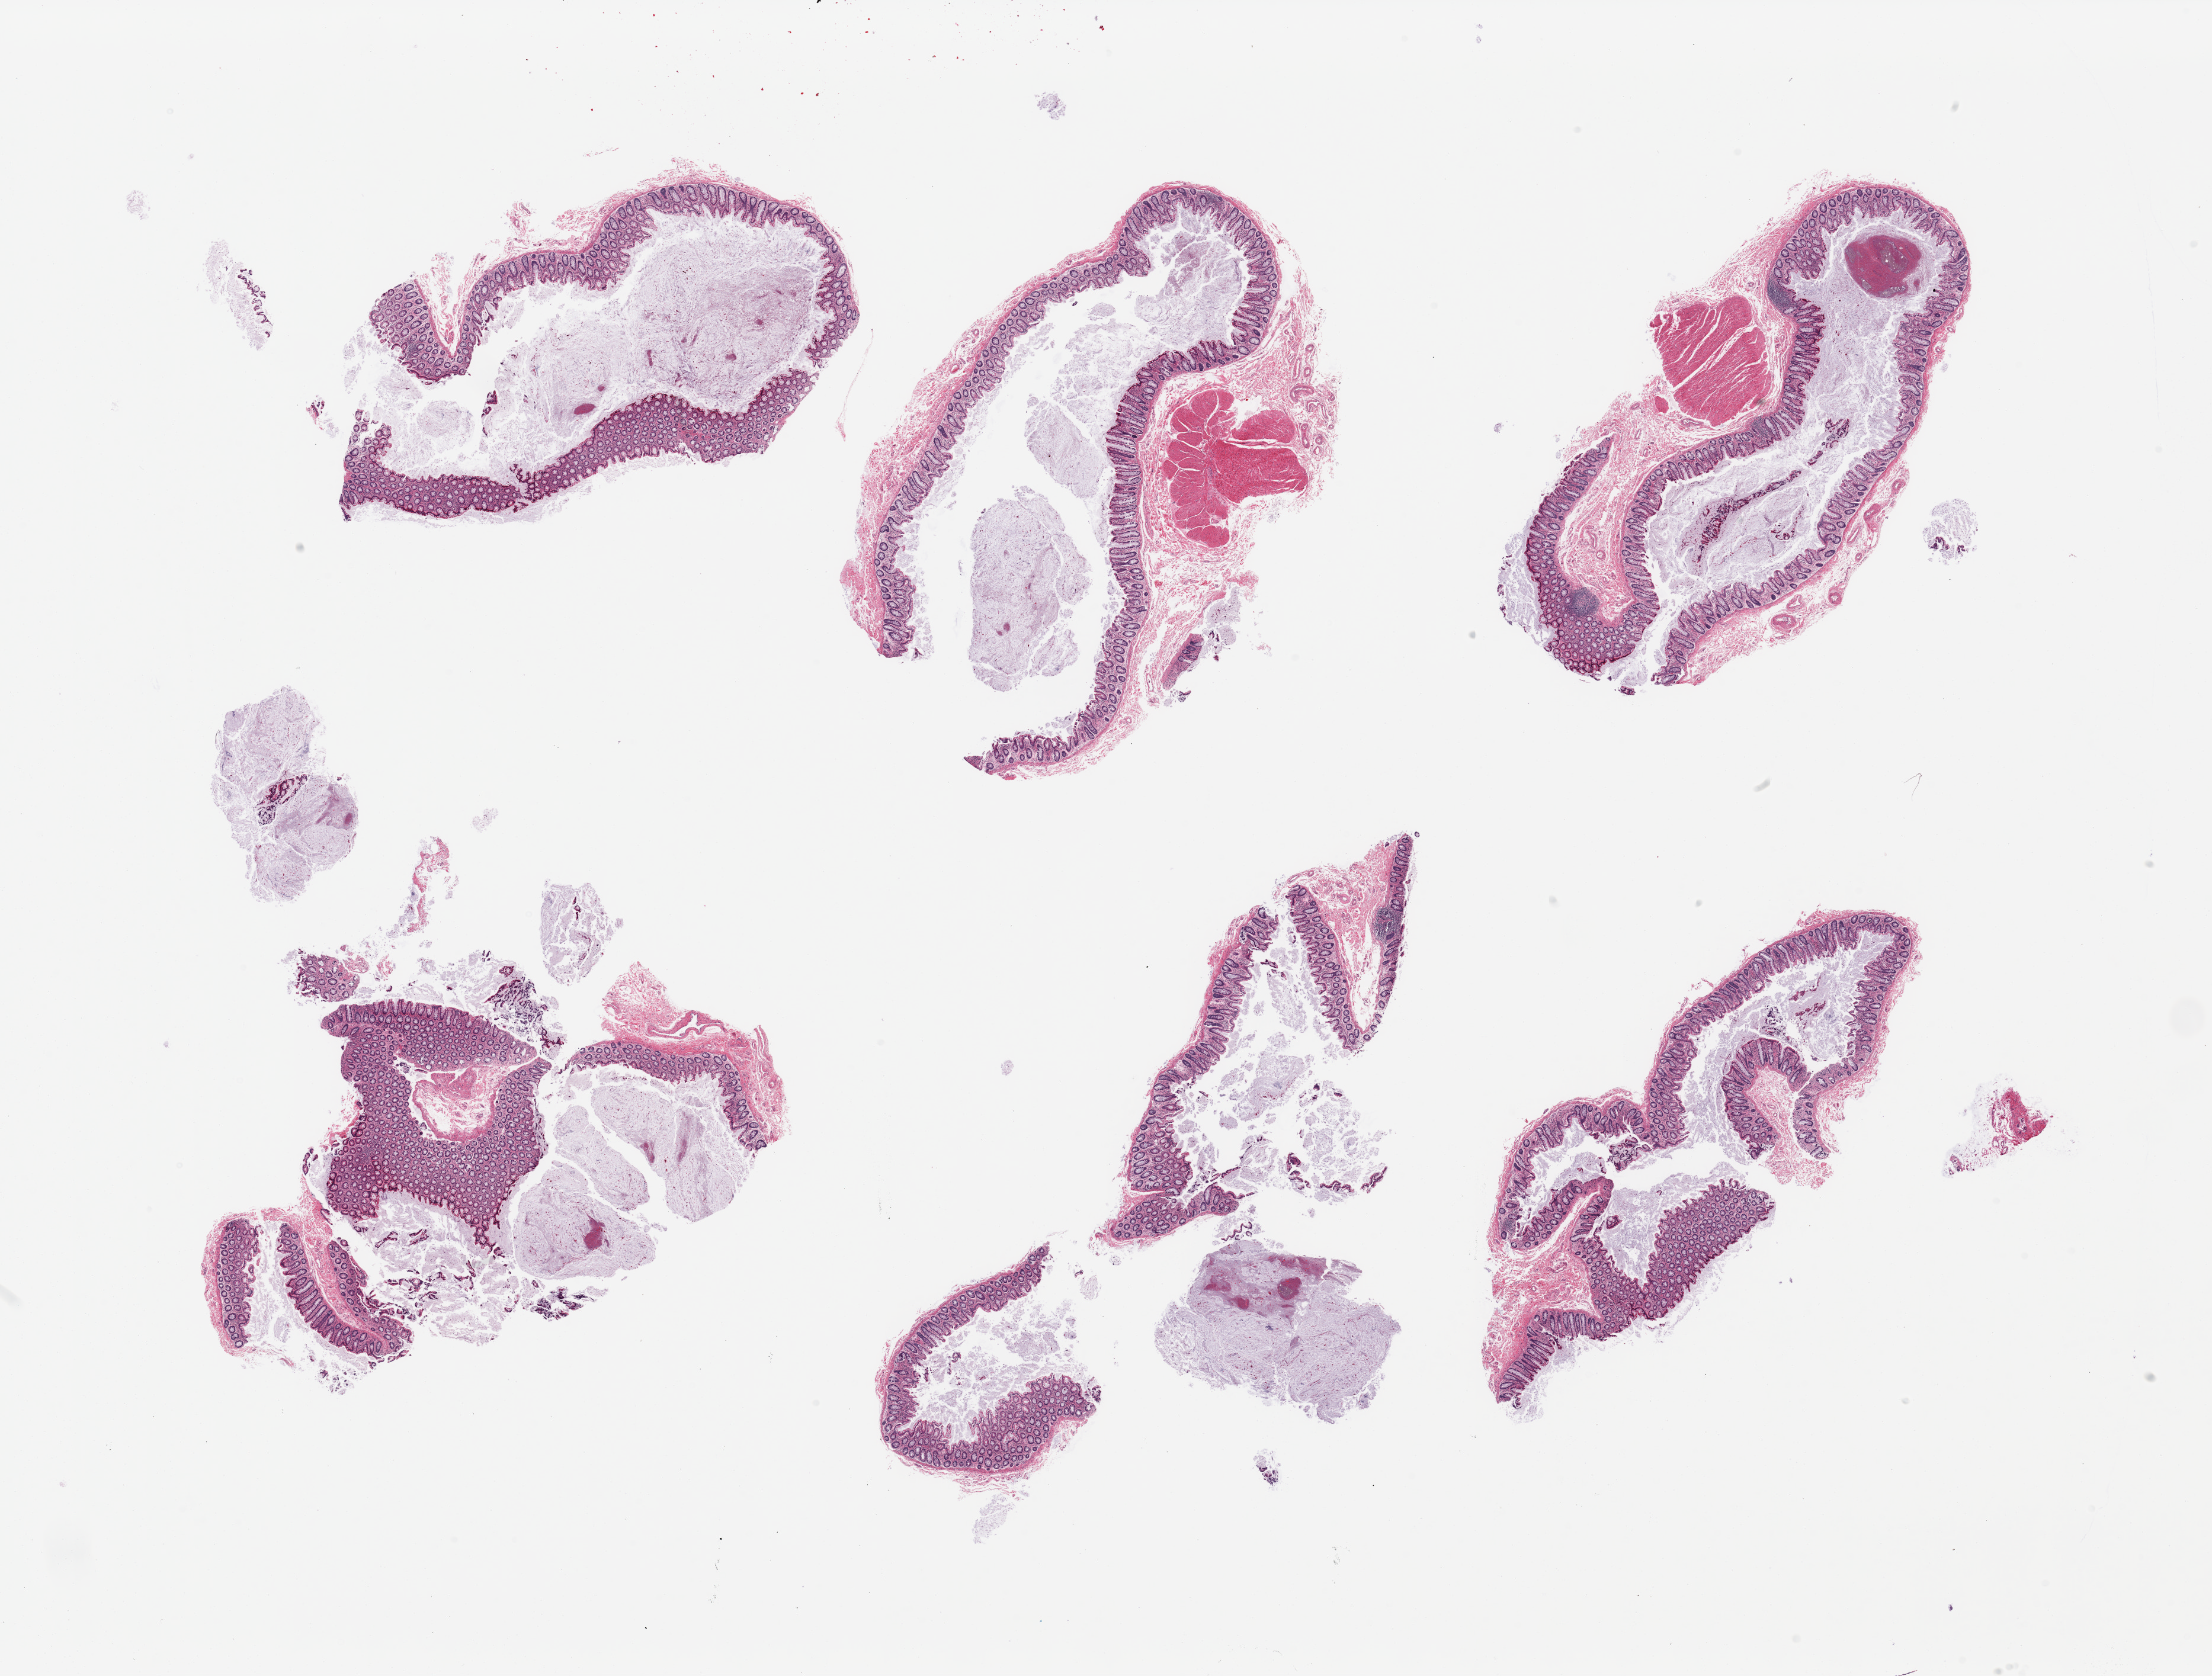
H&E whole-slide image, low-resolution overview of the scanned area, about 29.5 x 22.4 mm (slide scanned at 20x), PAXgene-fixed paraffin-embedded (PFPE) section, sampled site (target tissue): ileum, tissue donor sample. Donor: female.
Pathologist's review note for this sample: 6 pieces; colon not ileum.